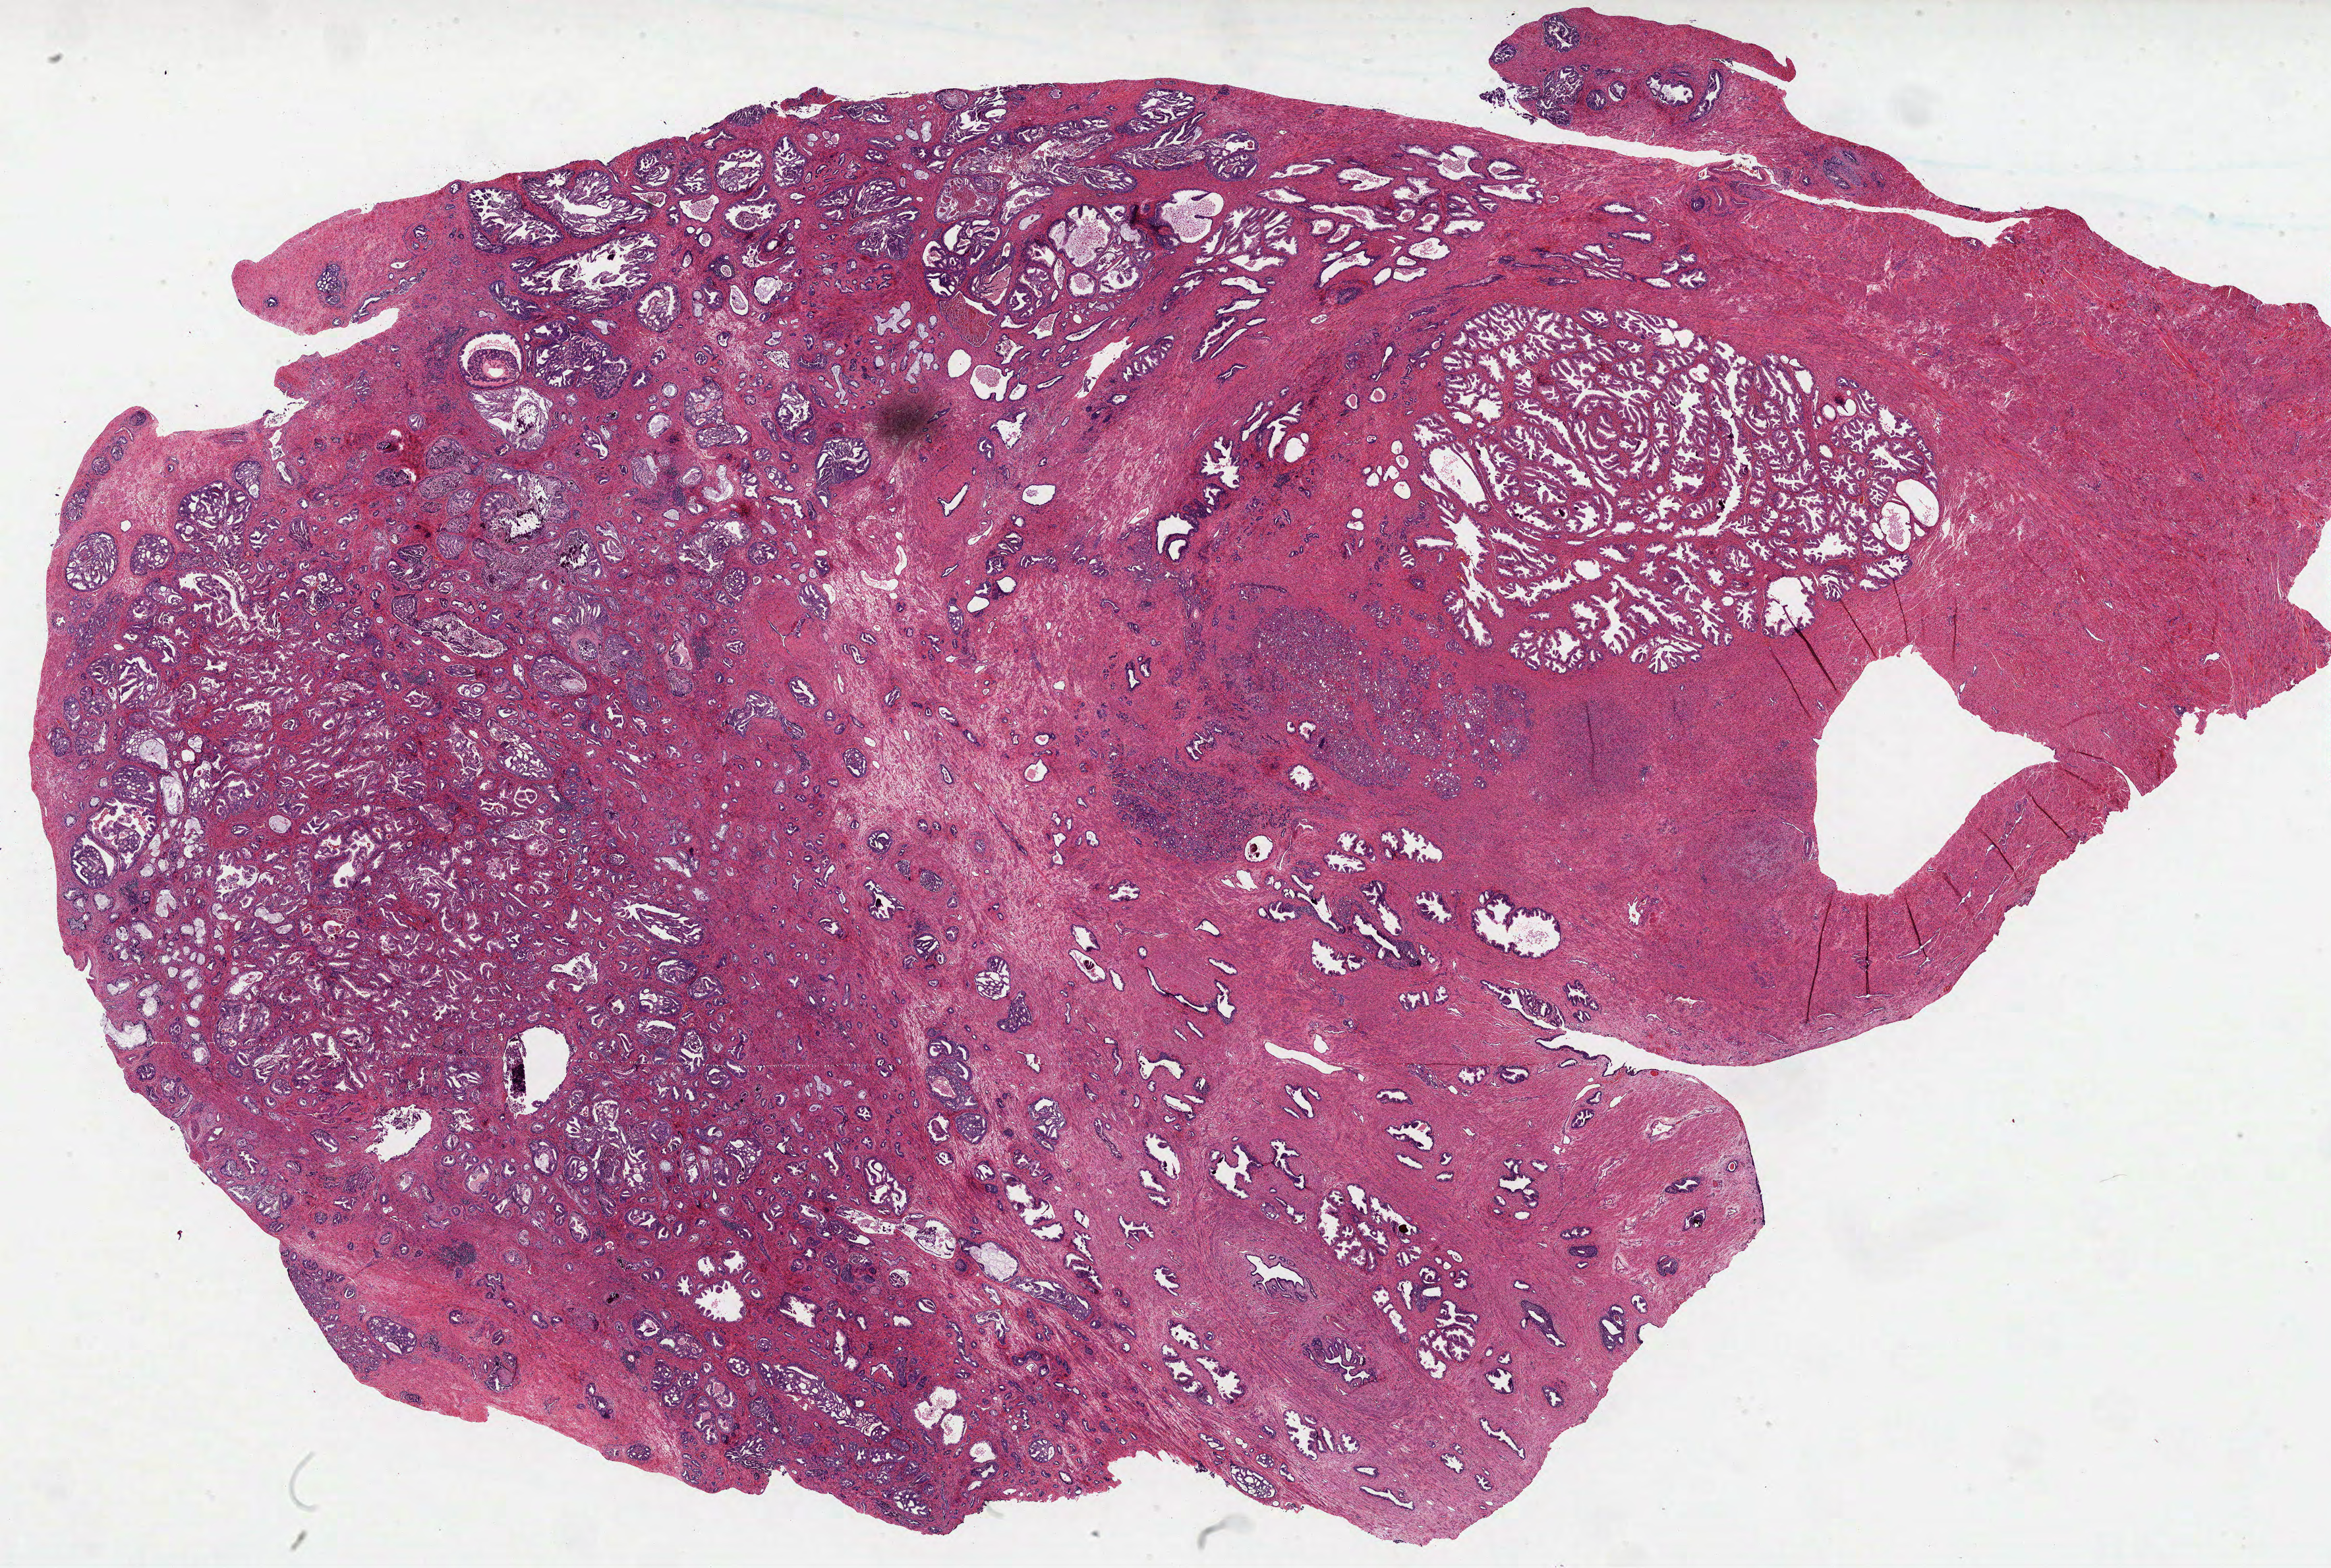
H&E-stained whole-slide image, a low-resolution overview of the entire scanned area, about 28.5 x 19.2 mm (acquisition: 40x scan); formalin-fixed paraffin-embedded (FFPE) diagnostic section; prostate, primary tumour sample. Male patient; age at initial diagnosis 62 years. Gleason score: 7 (4+3).
Lymph nodes positive (case pathology): 0 of 14 examined. Laterality: bilateral. Diagnosis: Acinar cell carcinoma.